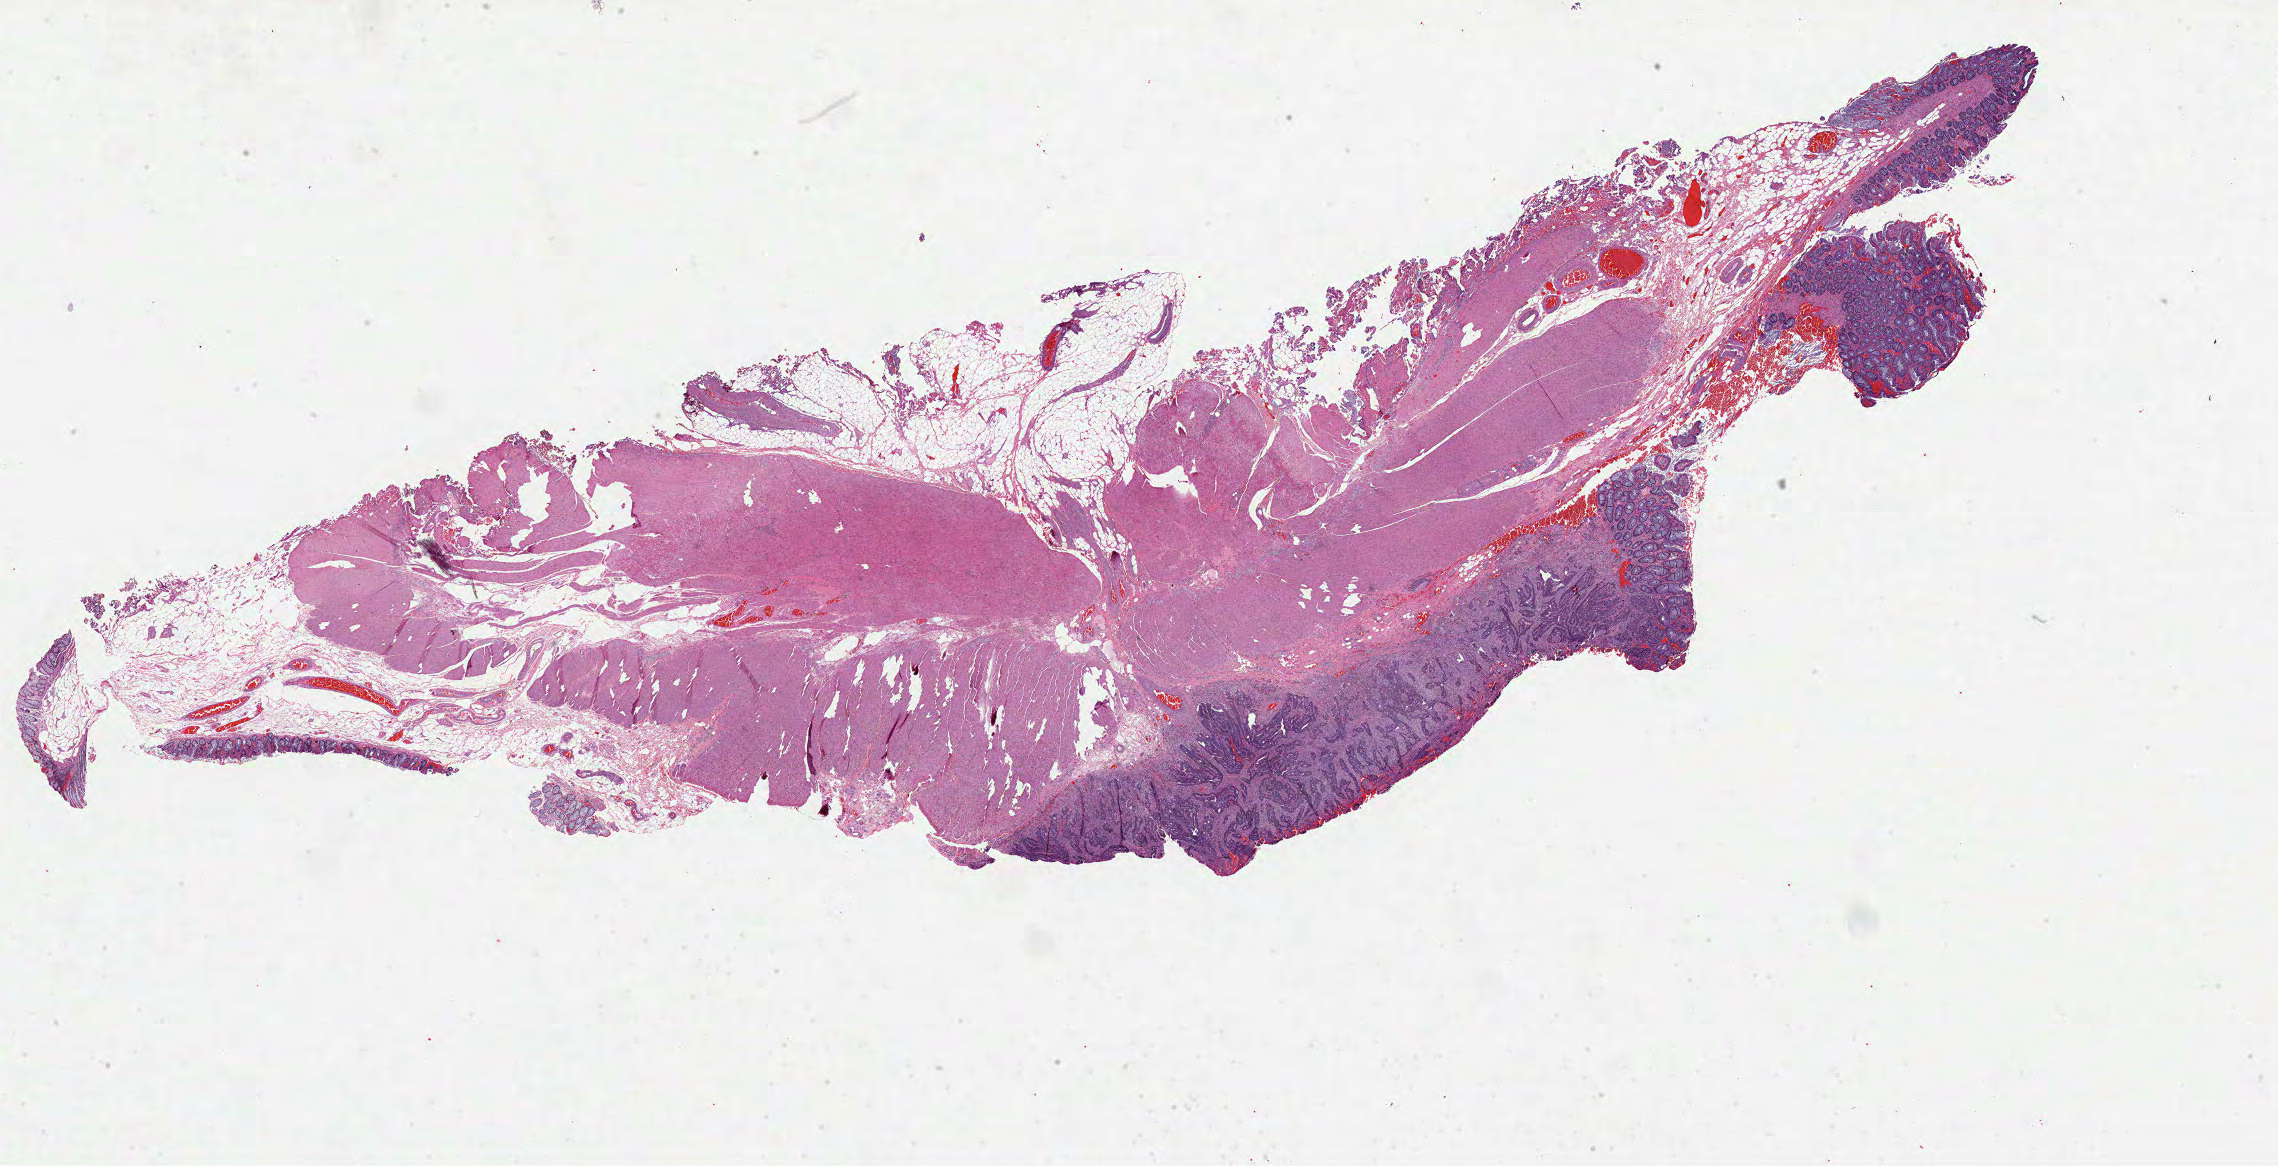
Whole-slide histology image, Hematoxylin and eosin (H&E) stained, shown as a low-resolution overview of the whole scanned area (about 36.7 x 18.8 mm). Formalin-fixed paraffin-embedded (FFPE) diagnostic section. Primary tumour sample from the rectum. Male patient; age at initial diagnosis 70 years.
Lymph nodes positive (case pathology): 0 of 1 examined. Histologic diagnosis: Adenocarcinoma, NOS. AJCC pathologic stage: I (7th edition). TNM: T2 N0 M0.